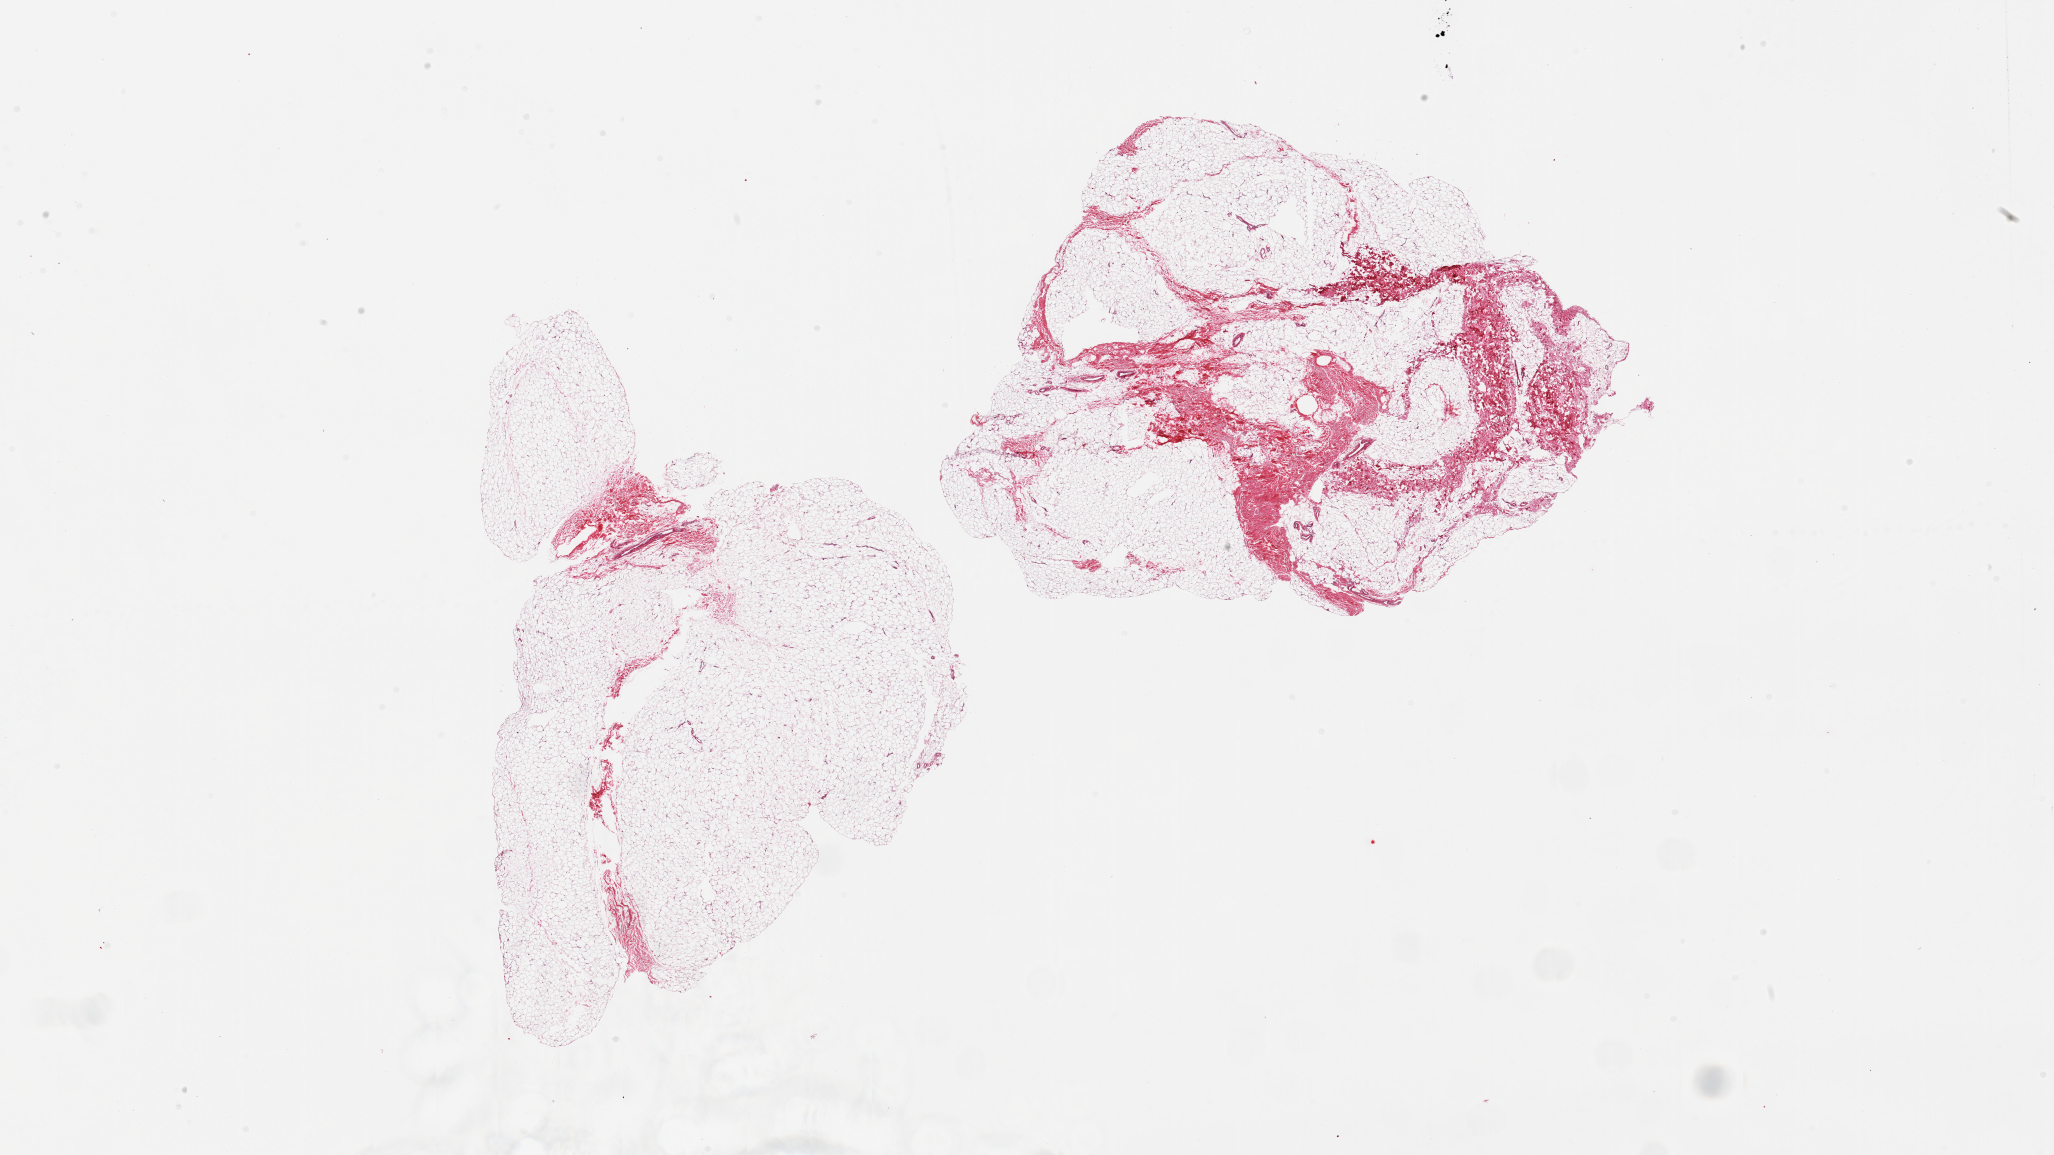
Digitized H&E-stained section, brightfield, a low-resolution overview of the entire scanned area, about 32.5 x 18.3 mm. PAXgene-fixed paraffin-embedded (PFPE) section. Sampled site (target tissue): breast. Donor tissue sample. Male donor.
• reviewer comment on this tissue sample: 2 pieces; fat and fibrous tissue (10-30%), no ductal elements seen